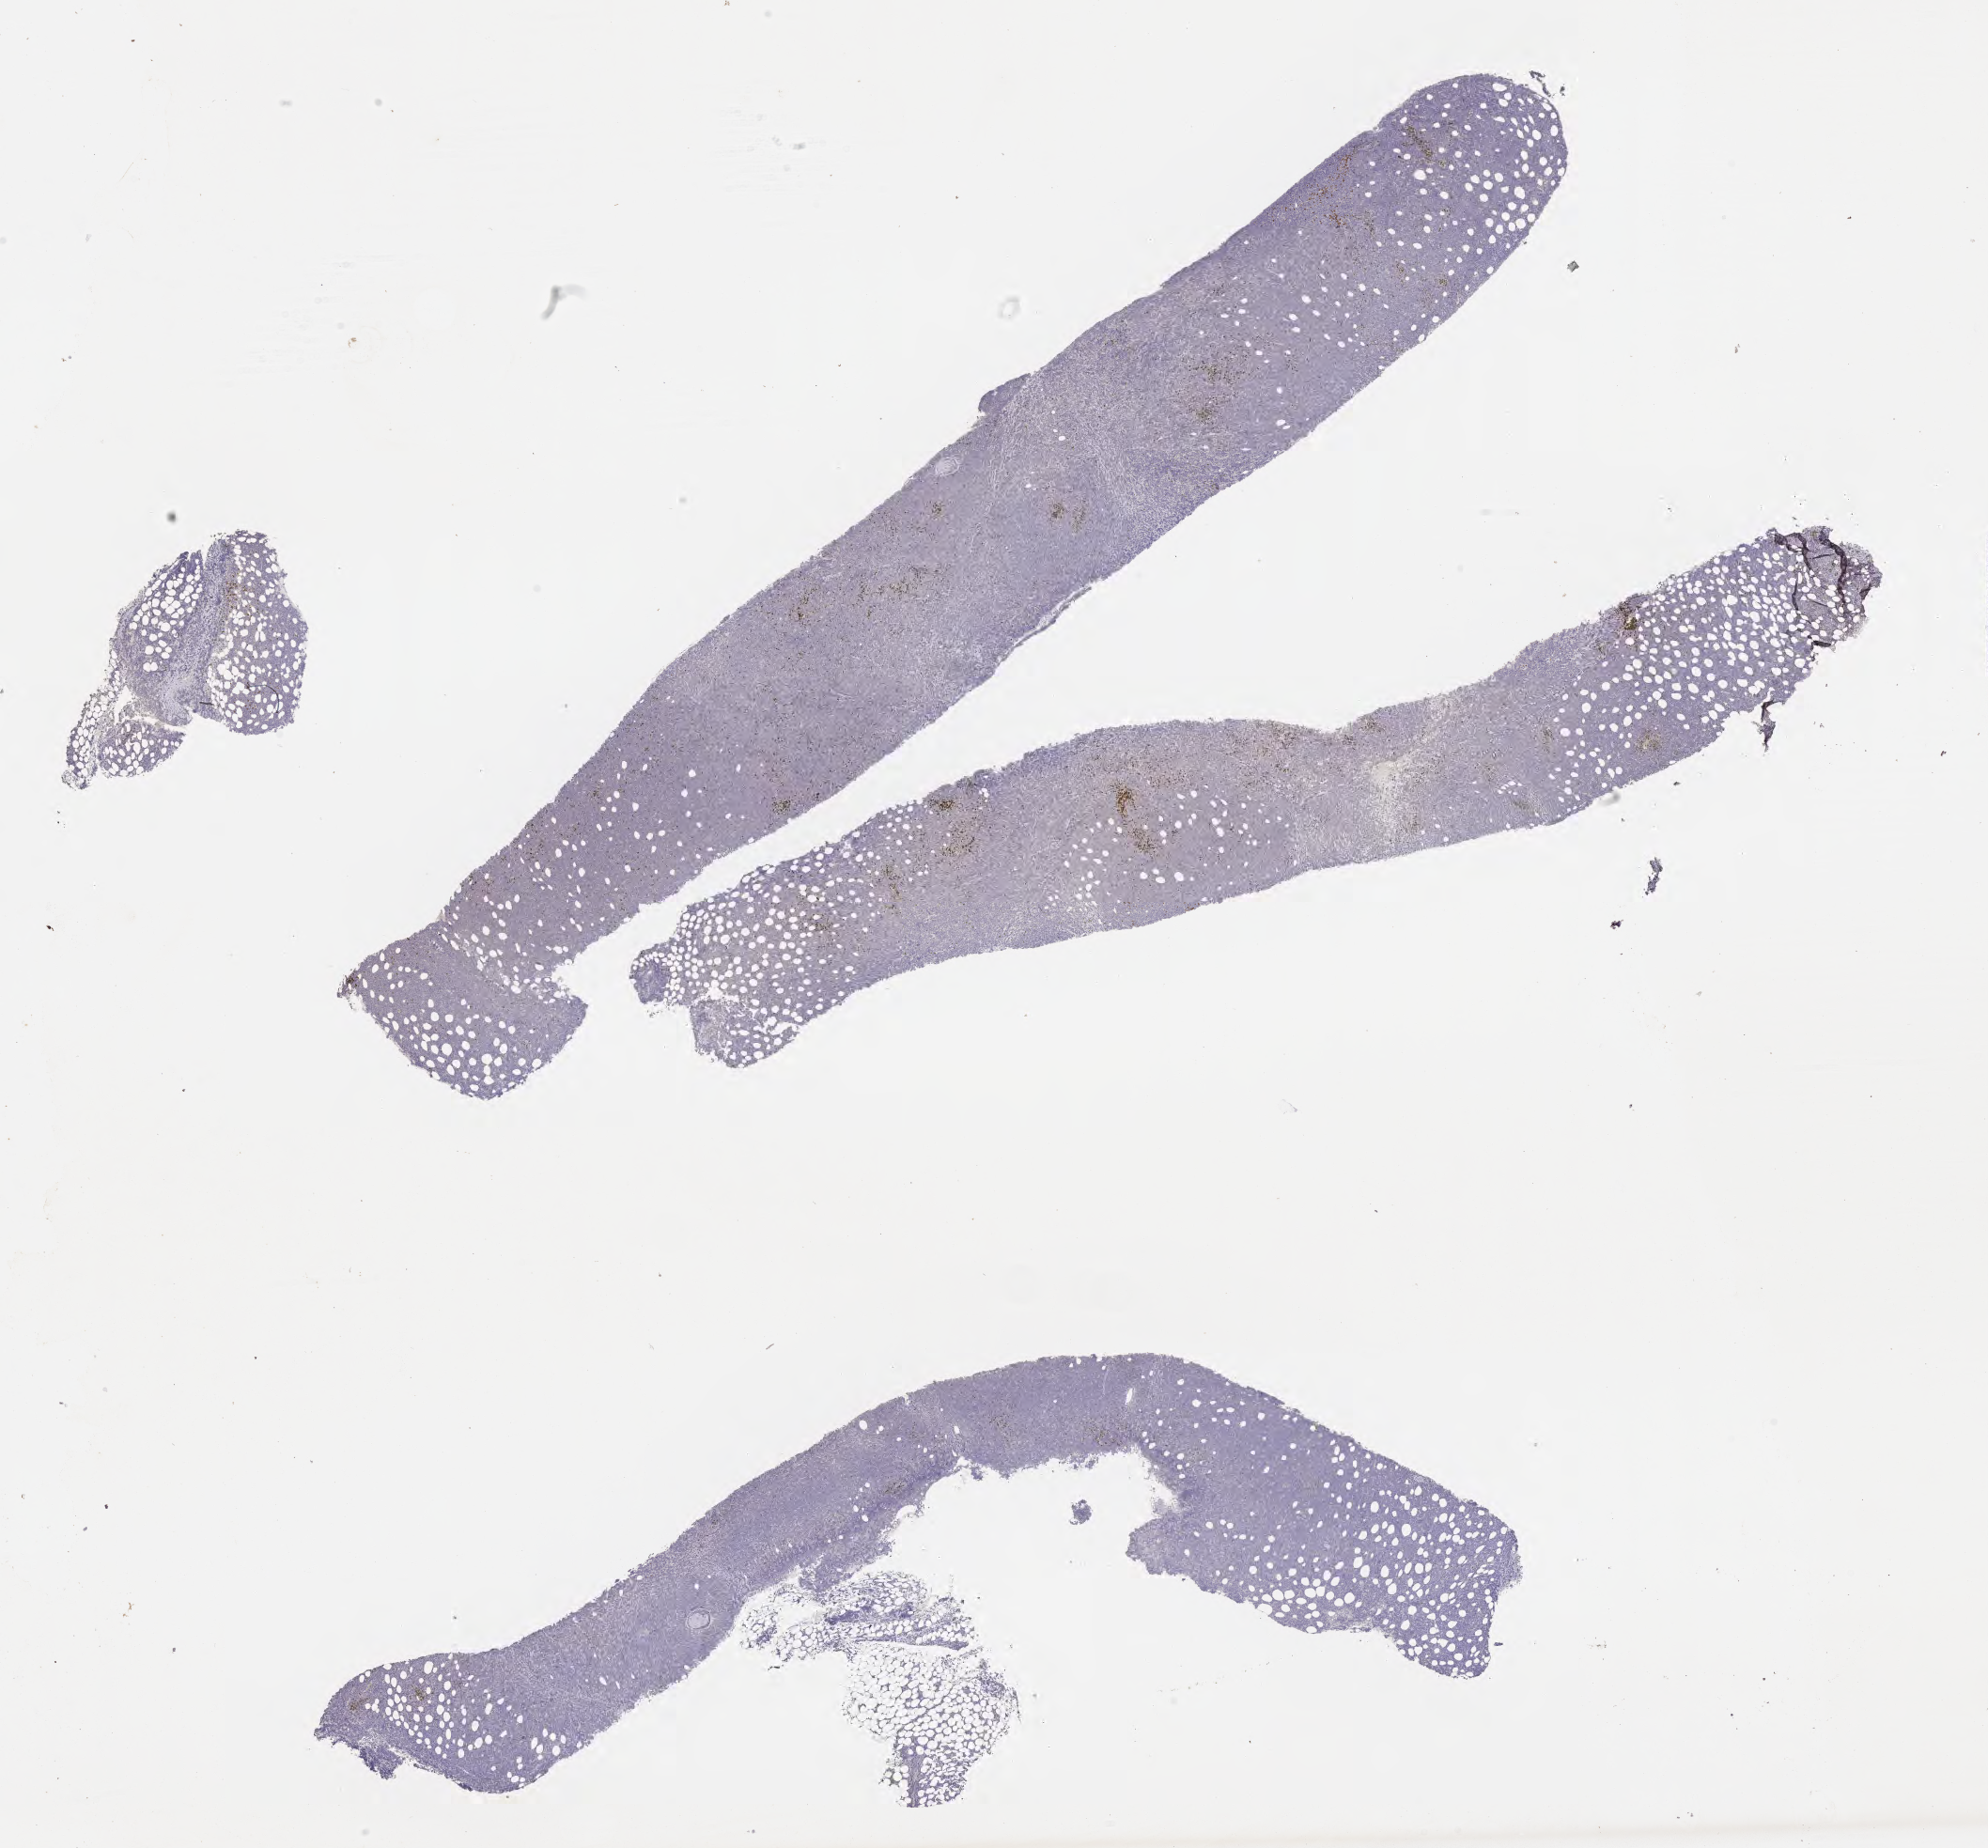
Whole-slide image, immunohistochemical stain for CD5, a low-resolution overview of the entire scanned area, about 17.1 x 15.9 mm; tumor tissue. Female patient, aged 43.
Histologic diagnosis: Burkitt lymphoma, NOS.